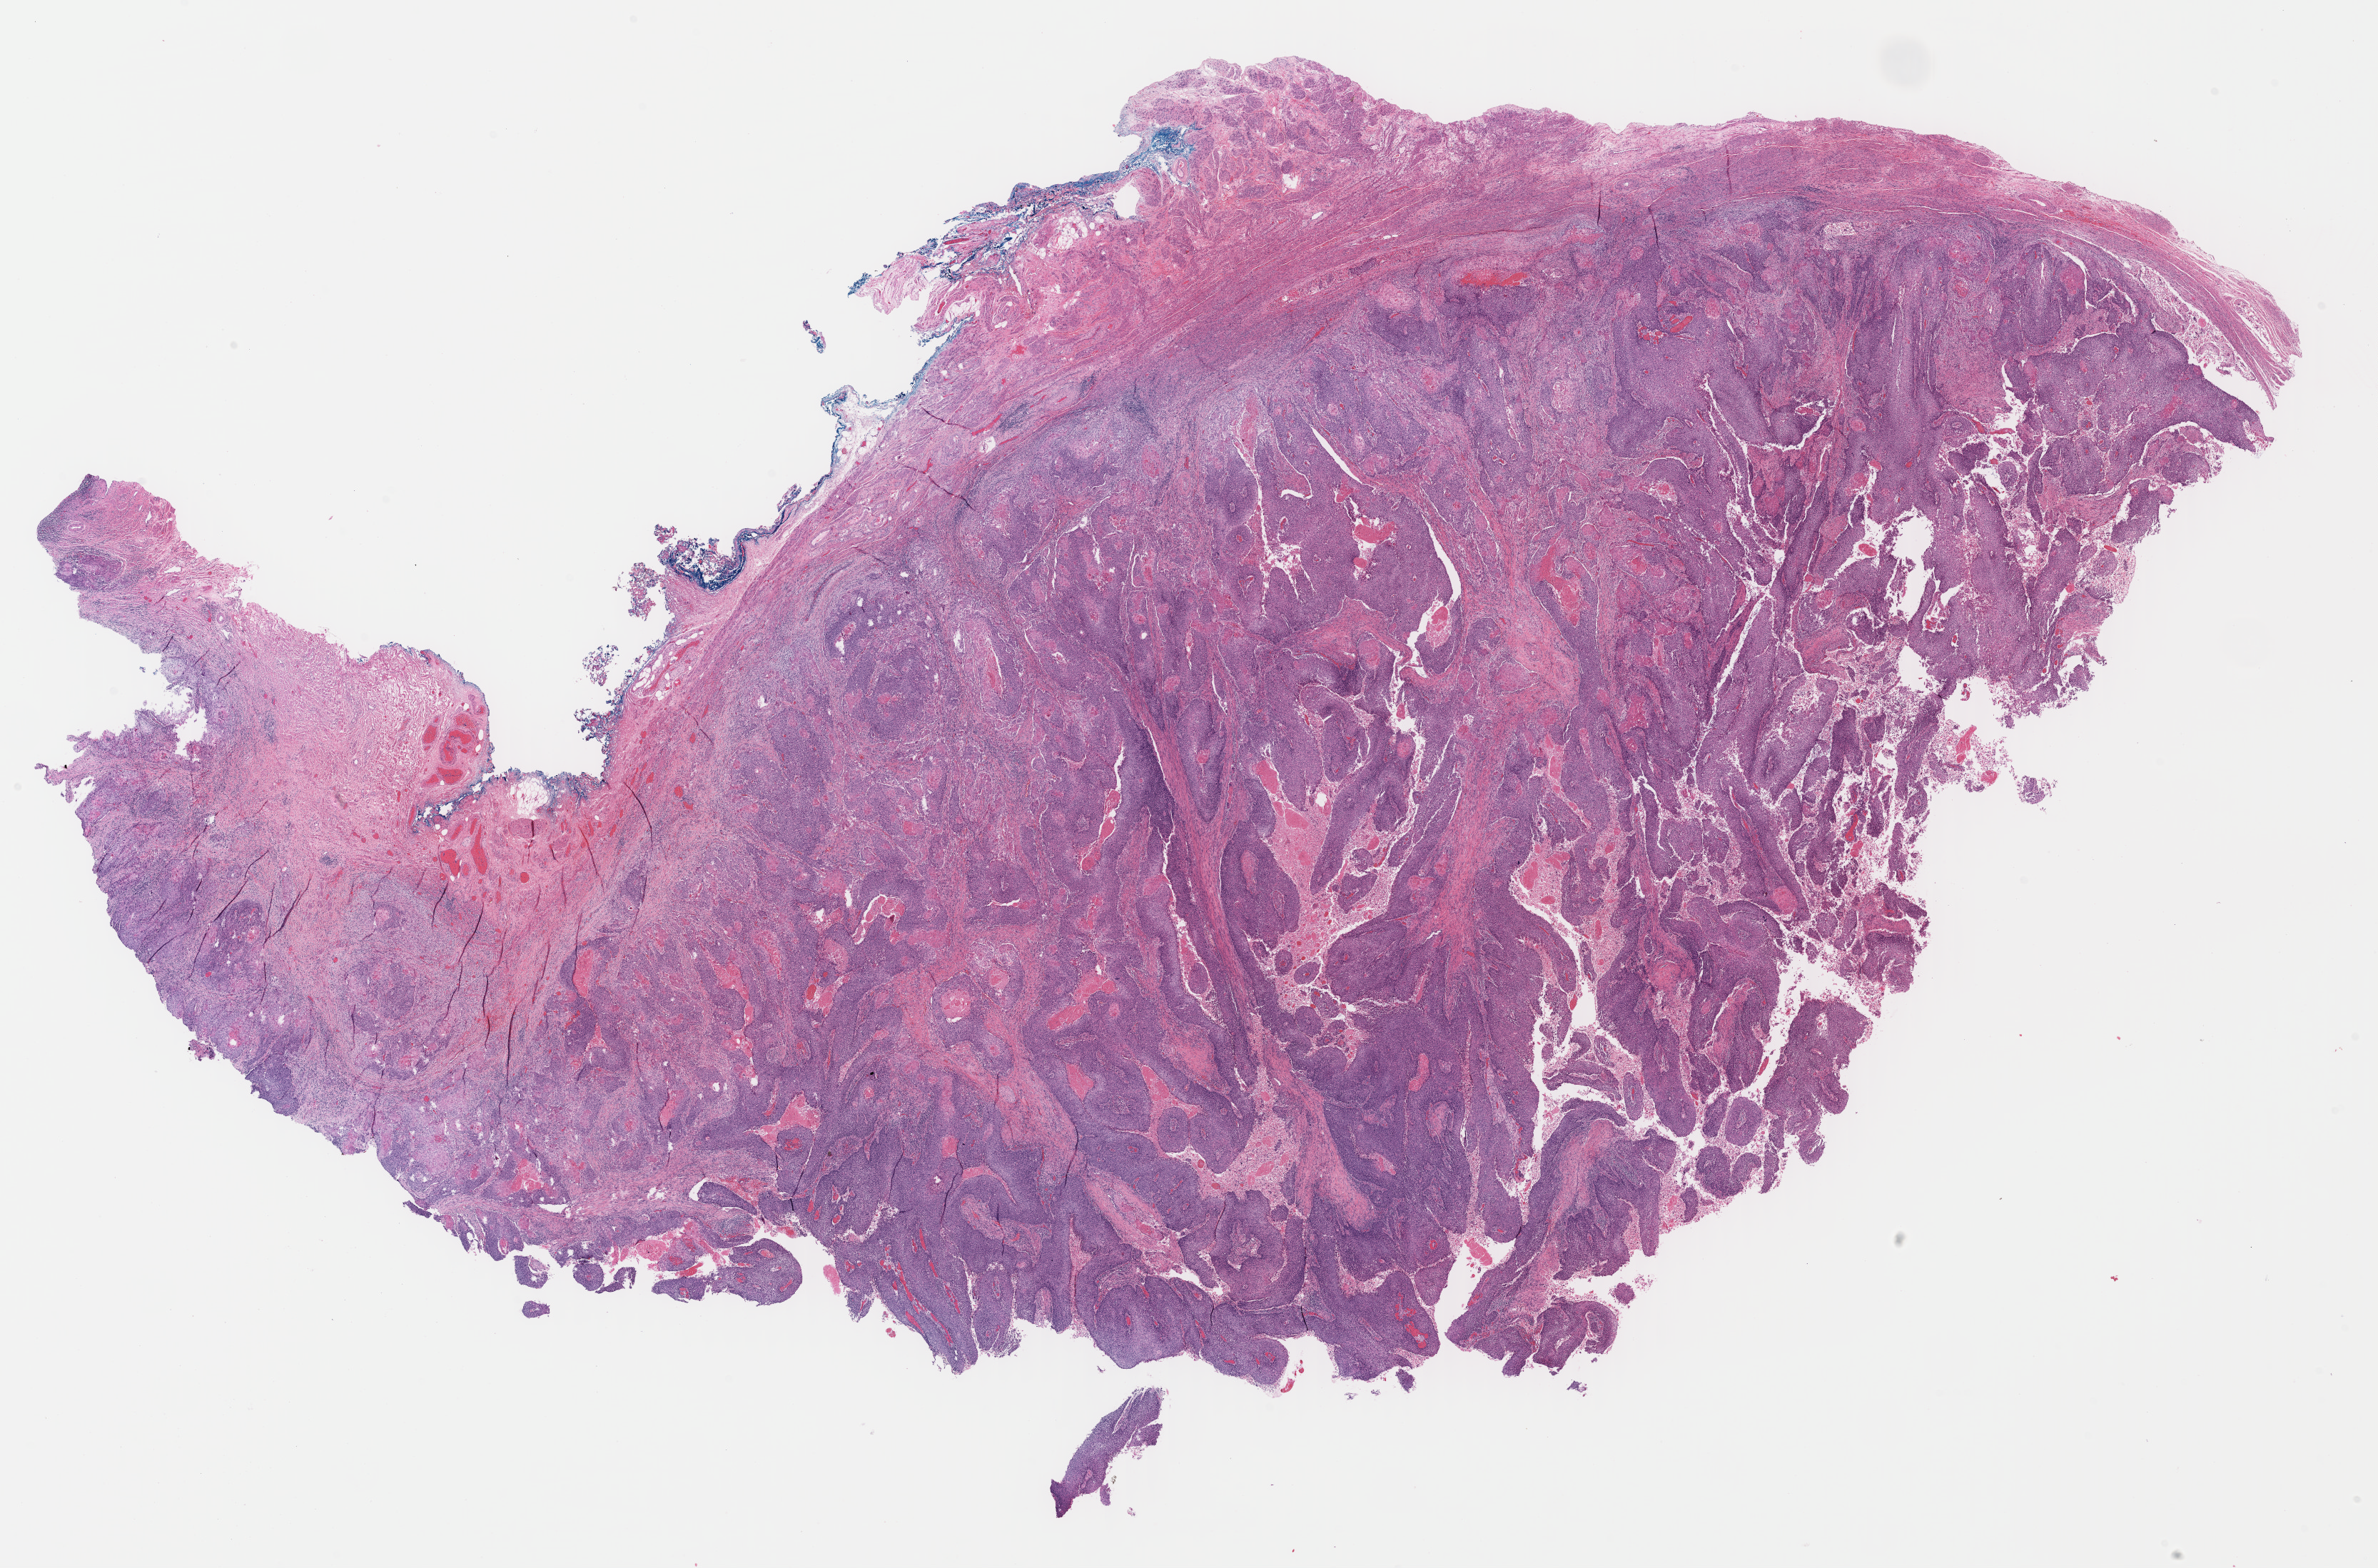
Whole-slide histology image, Hematoxylin and eosin (H&E) stained — a low-resolution overview of the entire scanned area, about 26.2 x 17.3 mm (slide scanned at 40x), FFPE section, primary tumour sample from the cervix. Female patient; age at initial diagnosis 68 years. Histologic grade: G1 (well differentiated).
FIGO stage: IIA2. Diagnosis: Squamous cell carcinoma, keratinizing, NOS (cervix uteri).